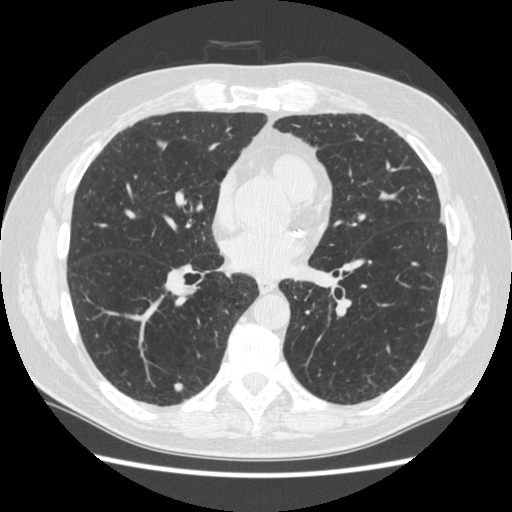
Low-dose screening chest CT, one axial slice. Slice 122 of 267 in the series (ordered by position). Reconstruction kernel STANDARD. 120 kVp. Lung window (W 1500 / L -600 HU). 512 × 512 image matrix.
Structures marked on this image (outlined manually by an expert reader):
- lesion 3 (nodule, lower lobe of right lung): bounding box <173,382,184,391> (left, top, right, bottom; pixels)